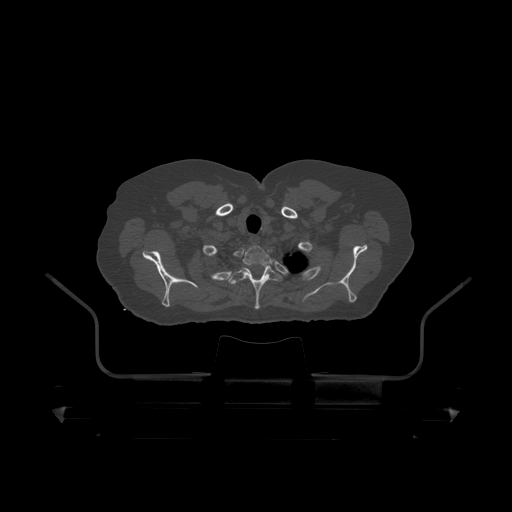
CT including the spine, one axial slice; position 381 of 390 along the scan axis; reconstruction kernel STANDARD; 120 kVp; bone window (W 1800 / L 400 HU); 512 × 512 image matrix, field of view 650 × 650 mm. Patient: male, 60 years. Case-level facts recorded for this patient, not image findings: primary cancer: prostate.
Outlined on this slice (semi-automatic segmentation, software-assisted and operator-edited):
- T1 vertebra: bounding box <214,246,272,267> (left, top, right, bottom; pixels)
- T2 vertebra: <229,265,282,310>